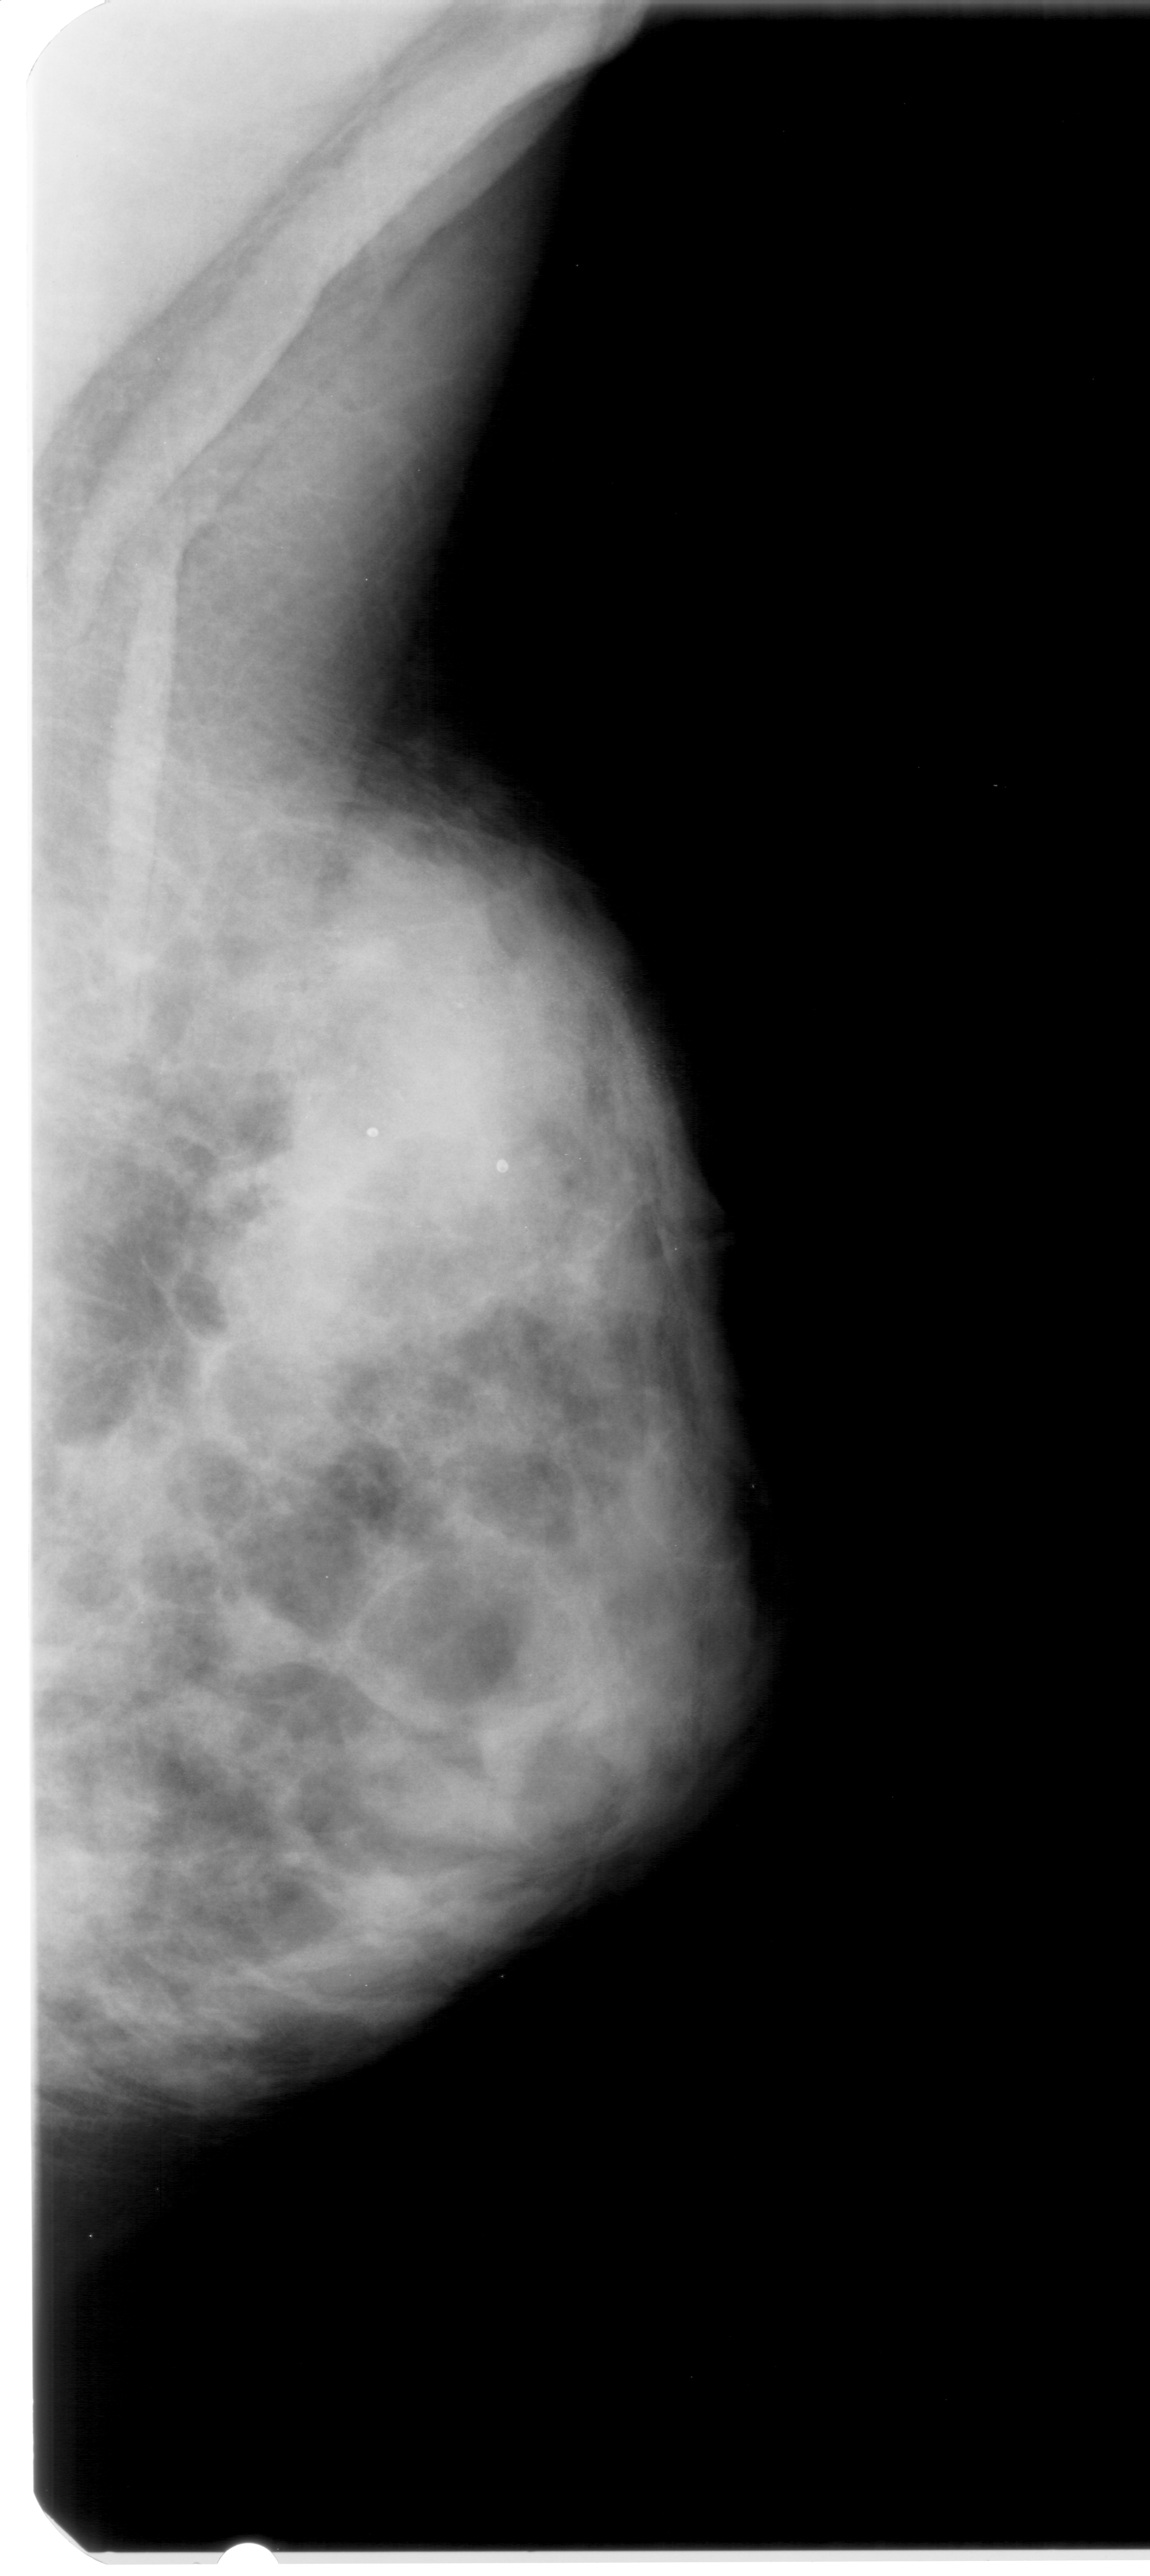
Mammogram (digitized film); right breast; MLO view; BI-RADS breast density category 4 (scale 1–4); 1150 × 2576 image matrix.
Expert-marked regions of interest on this image (one box per marked abnormality):
- calcifications, morphology punctate, distribution segmental; BI-RADS assessment category 4; subtlety rating 1 on a 1 (subtle) to 5 (obvious) scale; pathology (as recorded): benign: bounding box (x1, y1, x2, y2) in pixels: (293, 951, 578, 1161)